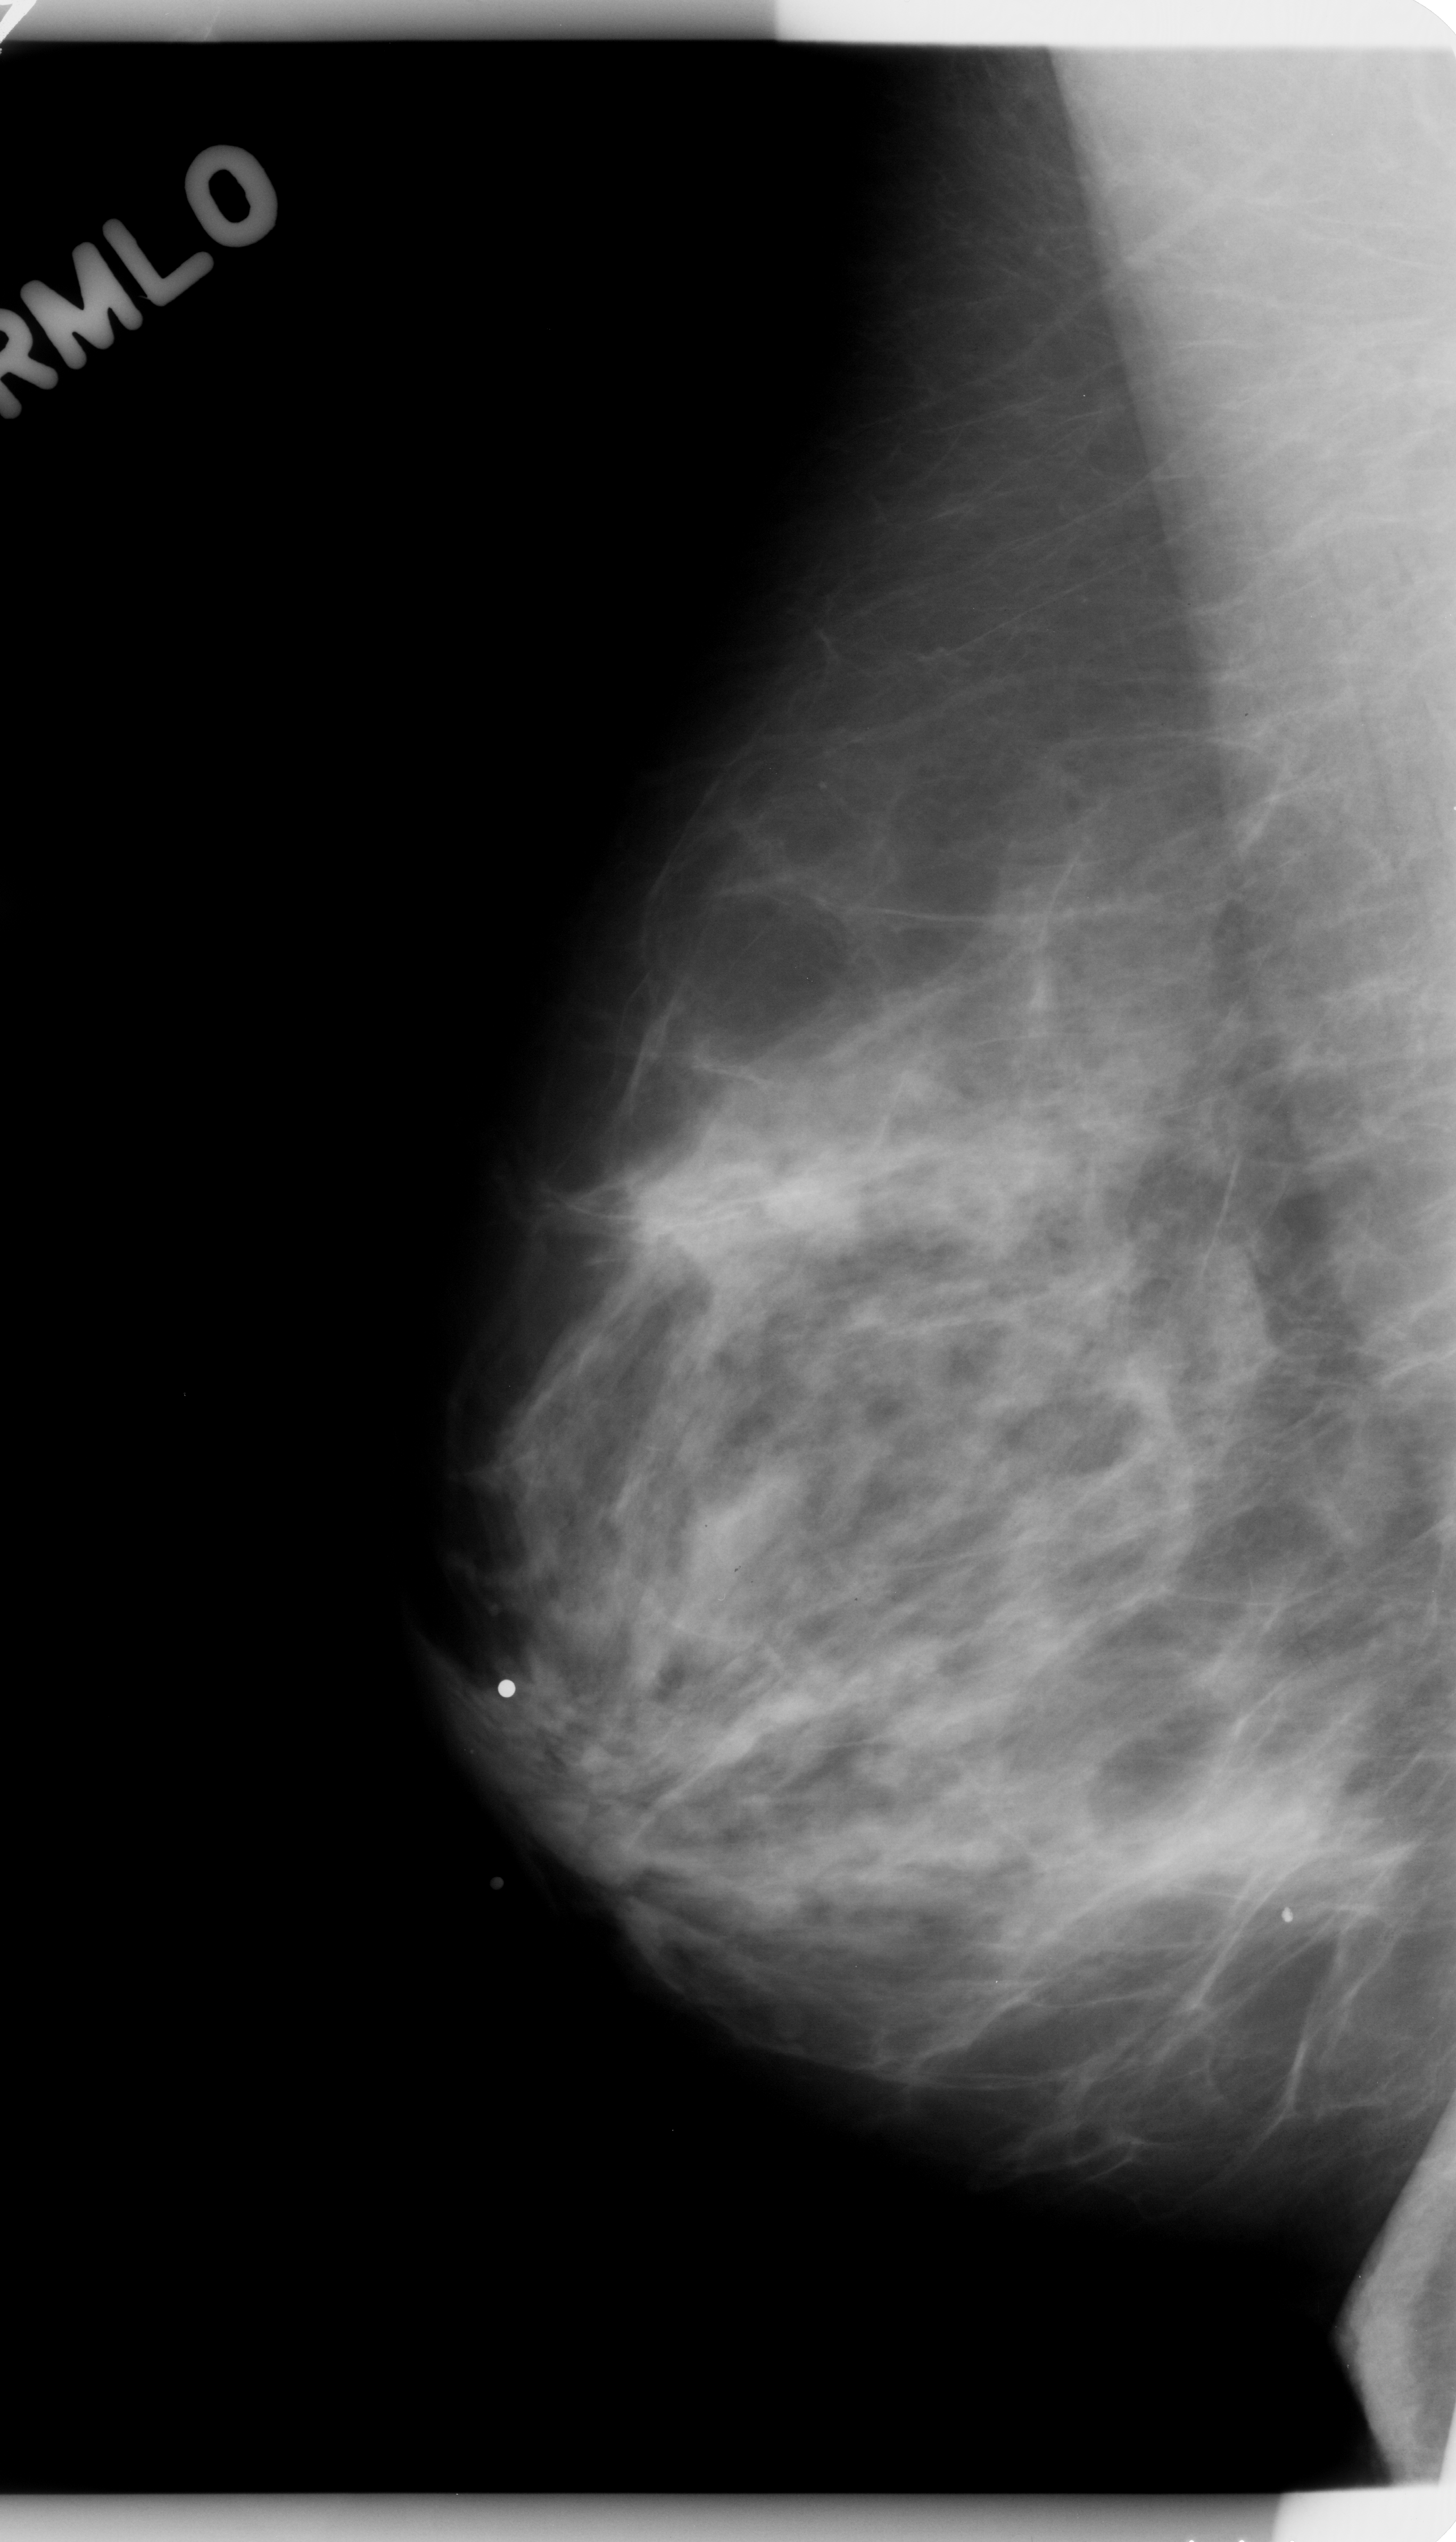
Digitized screen-film mammogram; right breast; MLO view; BI-RADS breast density category 2 (scale 1–4).
Marked findings (only marked abnormalities are described; nothing is implied about the rest of the image): mass, shape oval, margins circumscribed; BI-RADS assessment category 4; pathology (as recorded): benign.